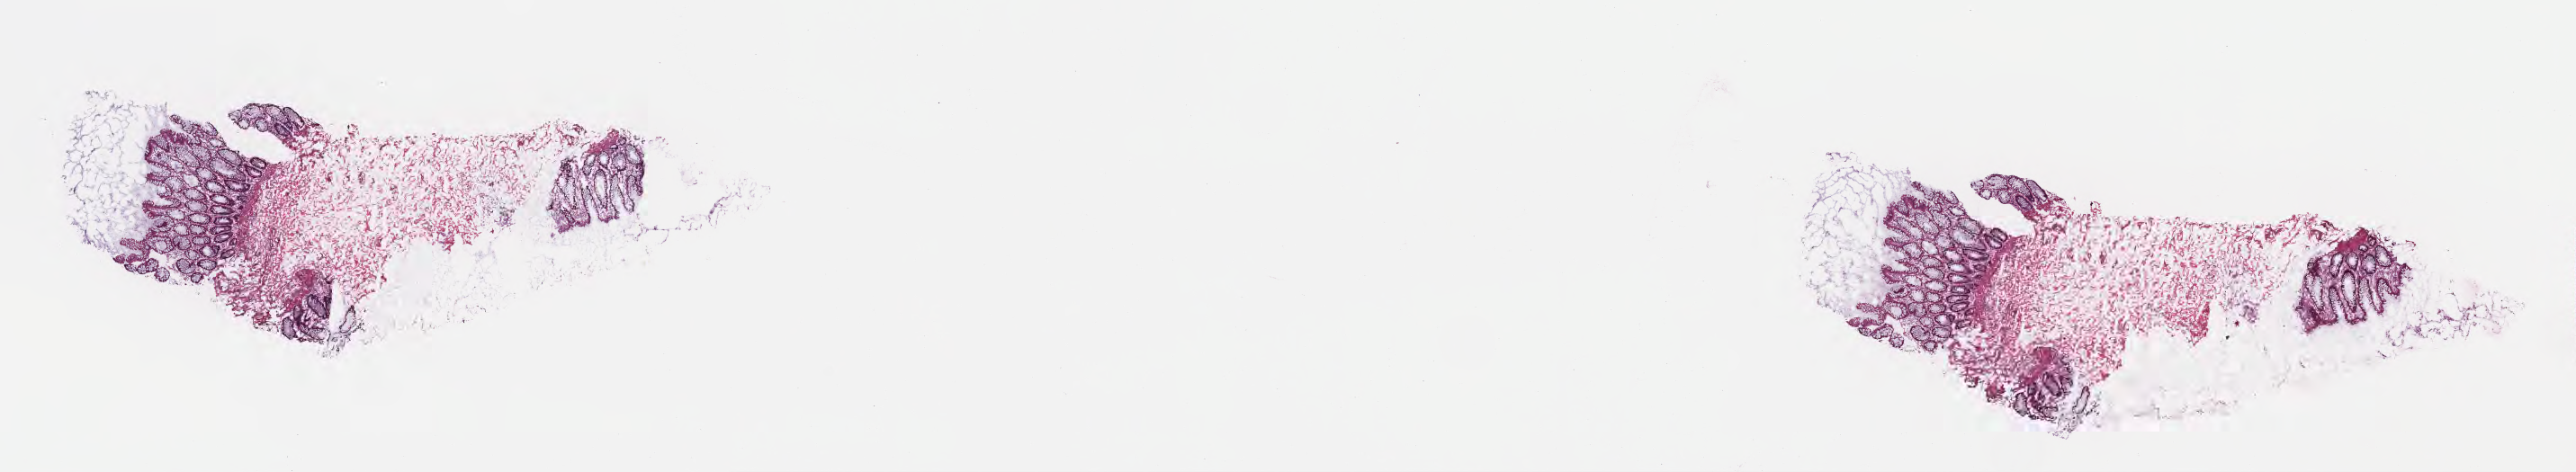
Hematoxylin and eosin (H&E) whole-slide image — shown as a low-resolution overview of the whole scanned area (about 23.1 x 4.2 mm), frozen section, metastatic tumor tissue, resected from liver. Male patient; age at initial diagnosis 72 years. Composition of this section per pathologist review: tumor cells 0%, tumor nuclei 0%.
Patient diagnosis (primary): Adenocarcinoma, NOS.